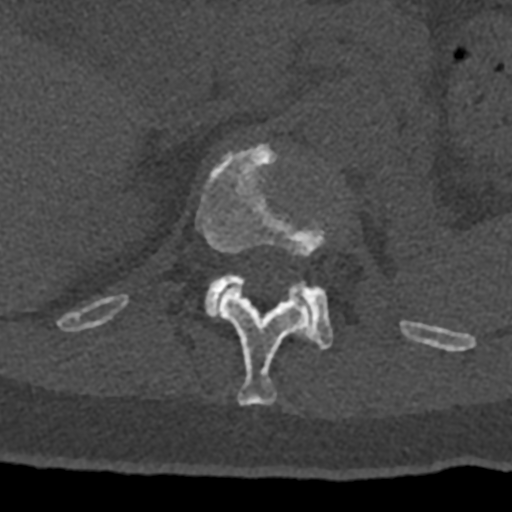
CT including the spine, one axial slice; slice 473 of 797 in the series (ordered by position); reconstruction kernel Br40s/3; 120 kVp; bone window (W 1800 / L 400 HU); 0.5 mm slice thickness; 512 × 512 image matrix, field of view 160 × 160 mm. Patient: male, 74 years. Case-level facts recorded for this patient, not image findings: primary cancer: renal; vertebrae with lytic lesions (as recorded): T10, L1, L2, L3, L4, L5.
Annotated regions visible in this slice (semi-automatically segmented with operator editing):
- L1 vertebra: bounding box <204,274,334,350> (left, top, right, bottom; pixels)
- T12 vertebra: <70,145,432,405>